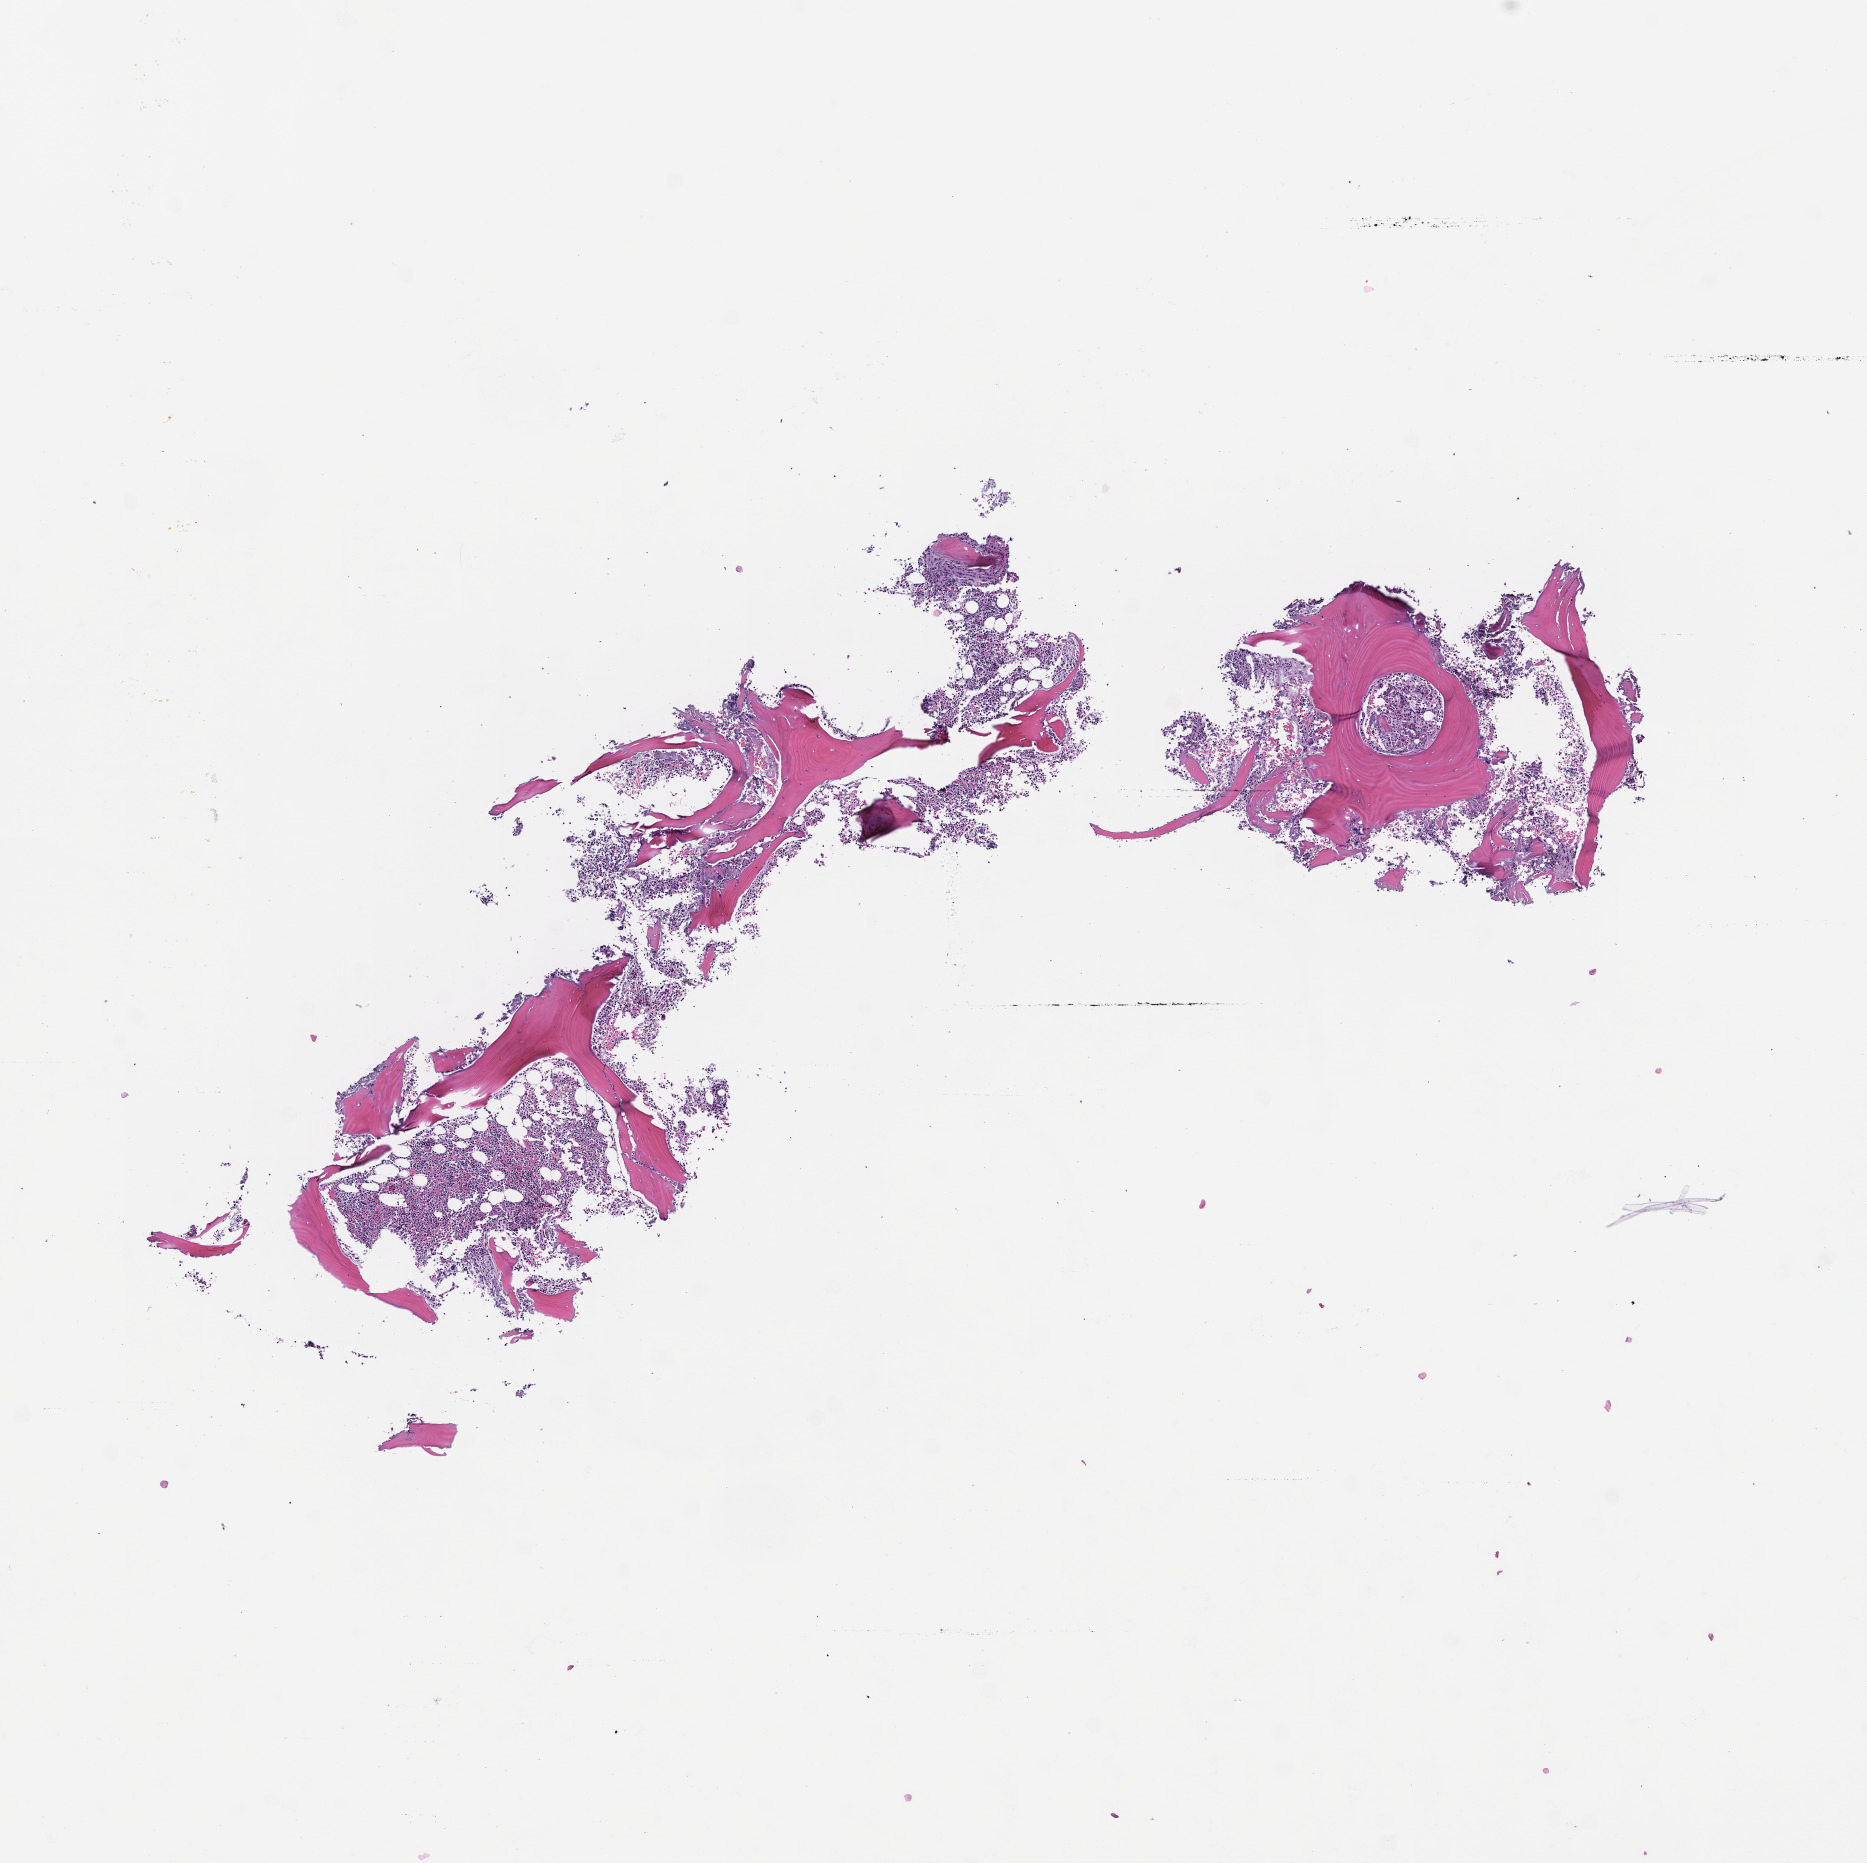
H&E whole-slide image, shown as a low-resolution overview of the whole scanned area (about 7.5 x 7.5 mm); formalin-fixed, paraffin-embedded (FFPE) tissue; tissue site: bone marrow. Patient sex: male.
This section: primary tumour tissue. Diagnosis: Plasma Cell Myeloma.